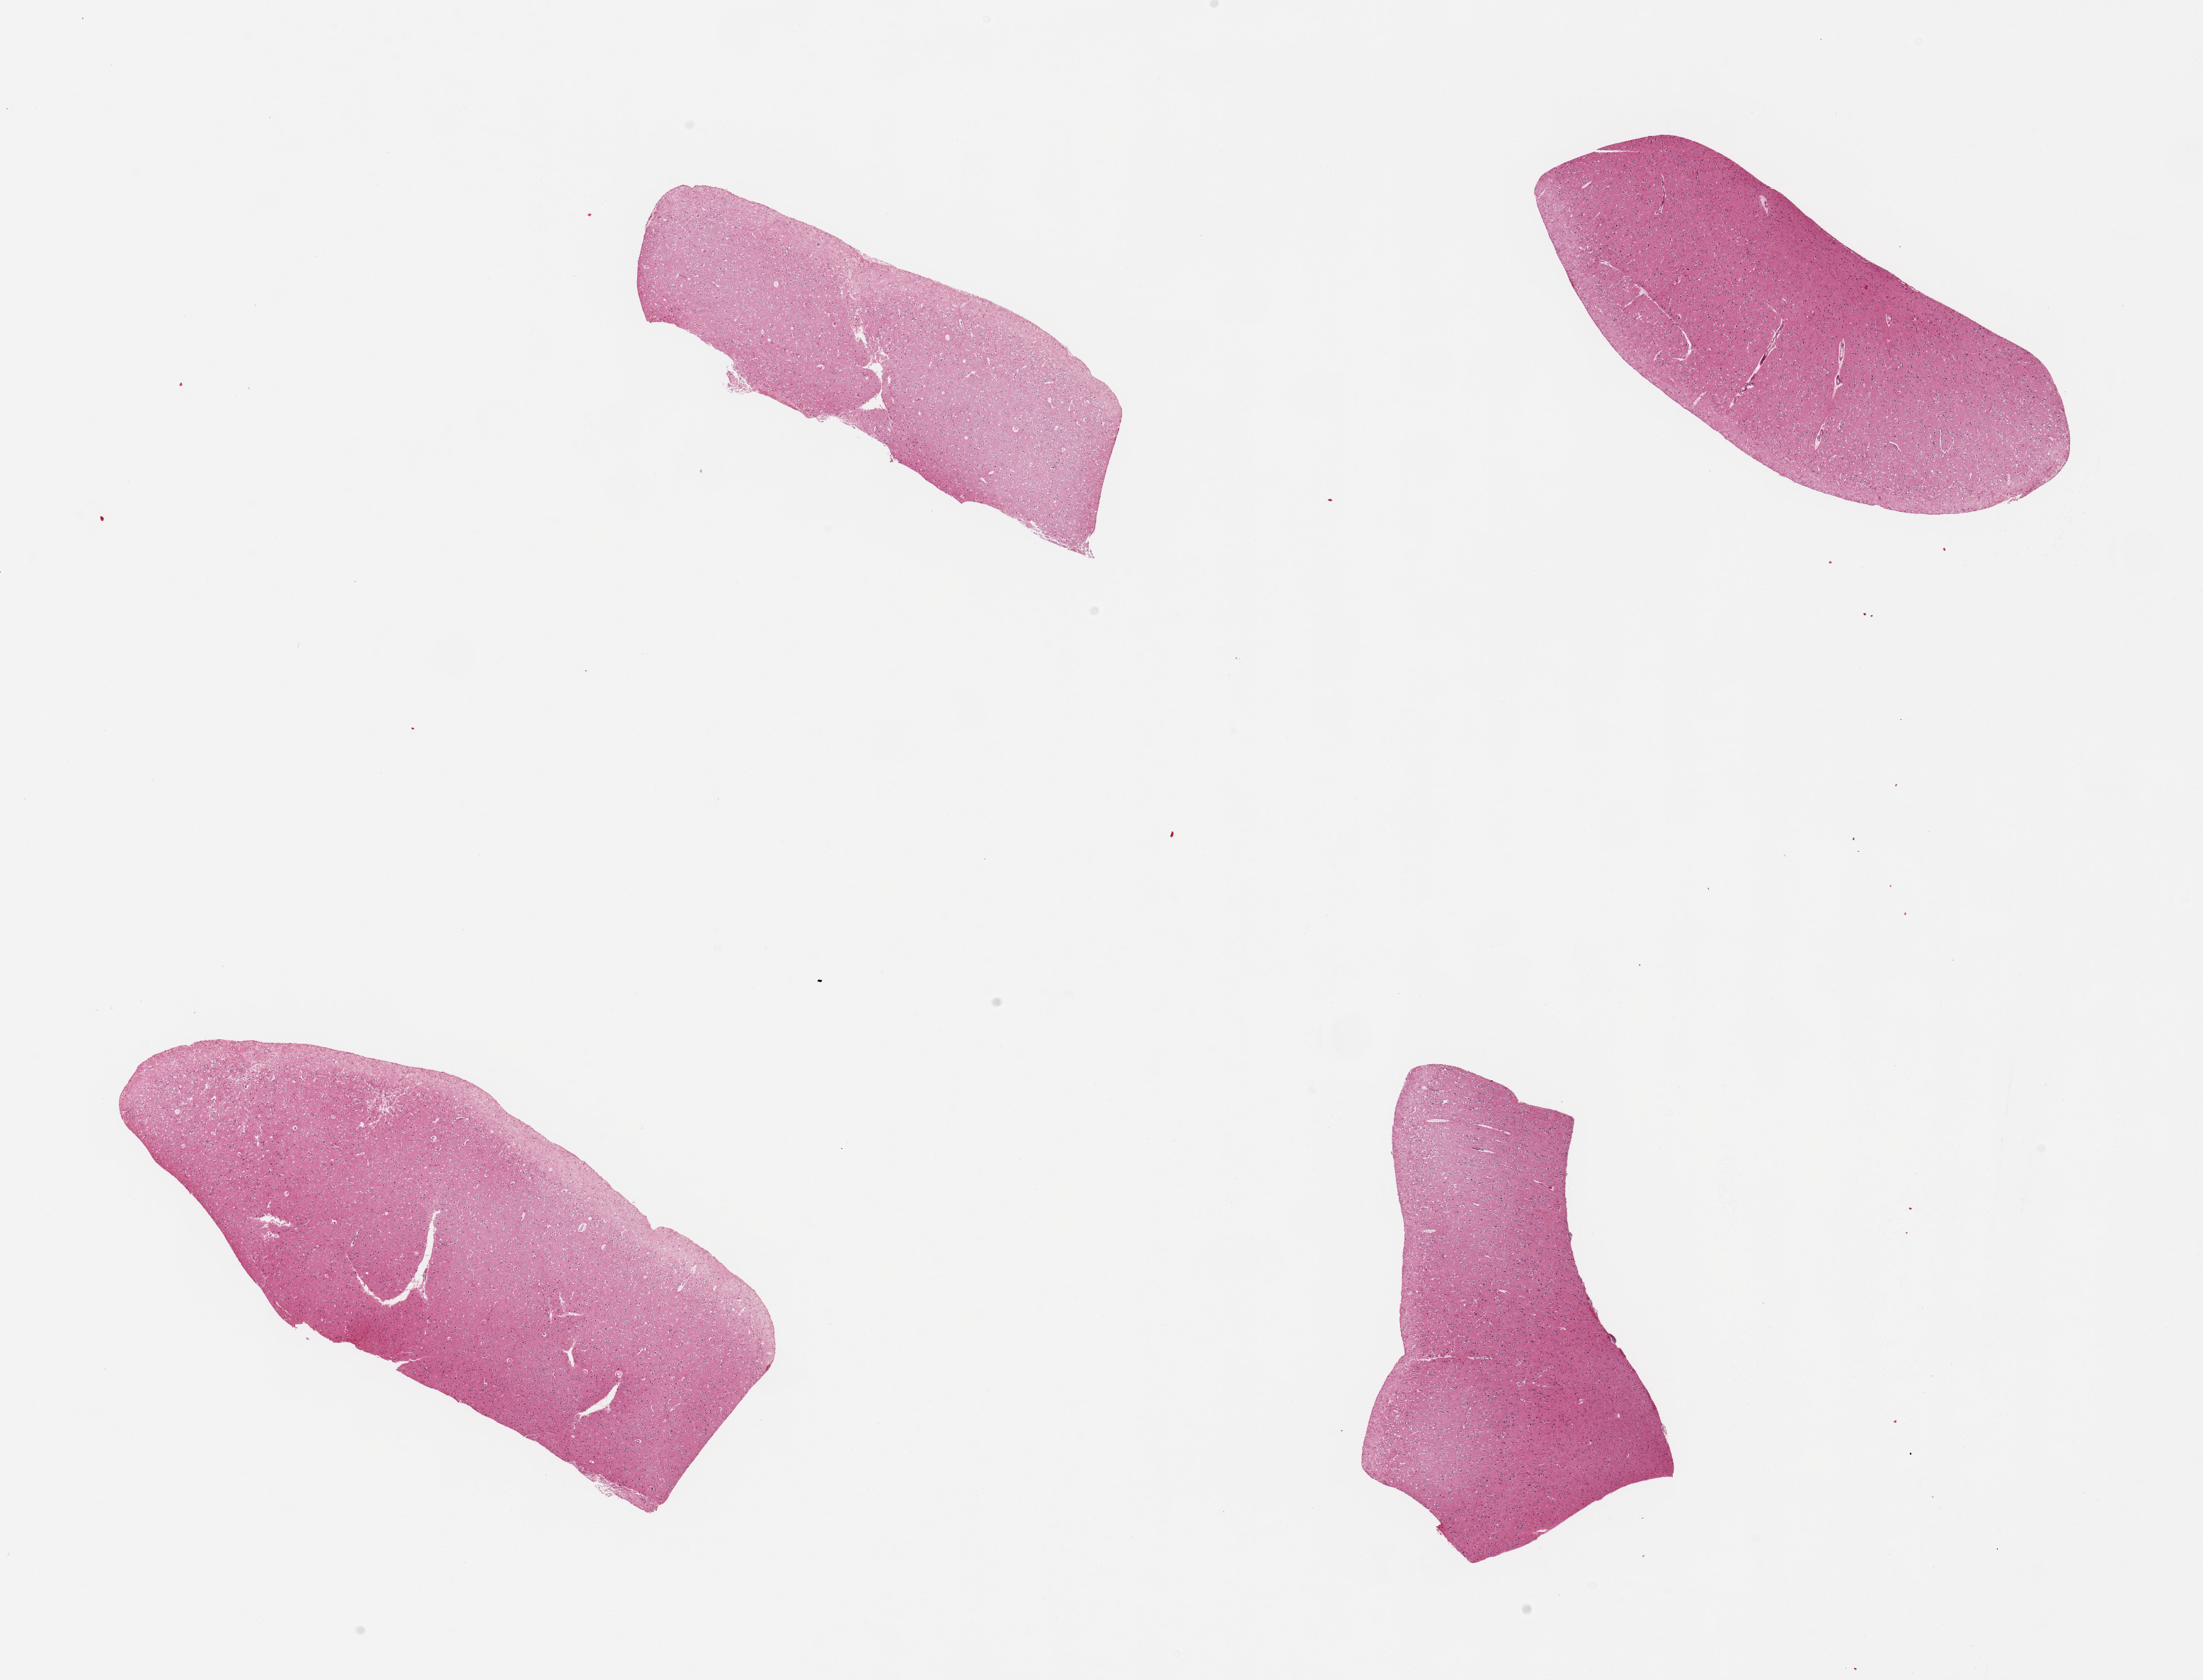
Whole-slide image, hematoxylin and eosin (H&E) stain, brightfield, a low-resolution overview of the entire scanned area, about 24.6 x 18.8 mm. PAXgene-fixed, paraffin-embedded tissue. Section of cerebral cortex (target tissue). Donor tissue sample. Male donor.
- reviewer comment on this tissue sample: 4 pieces, no abnormalities